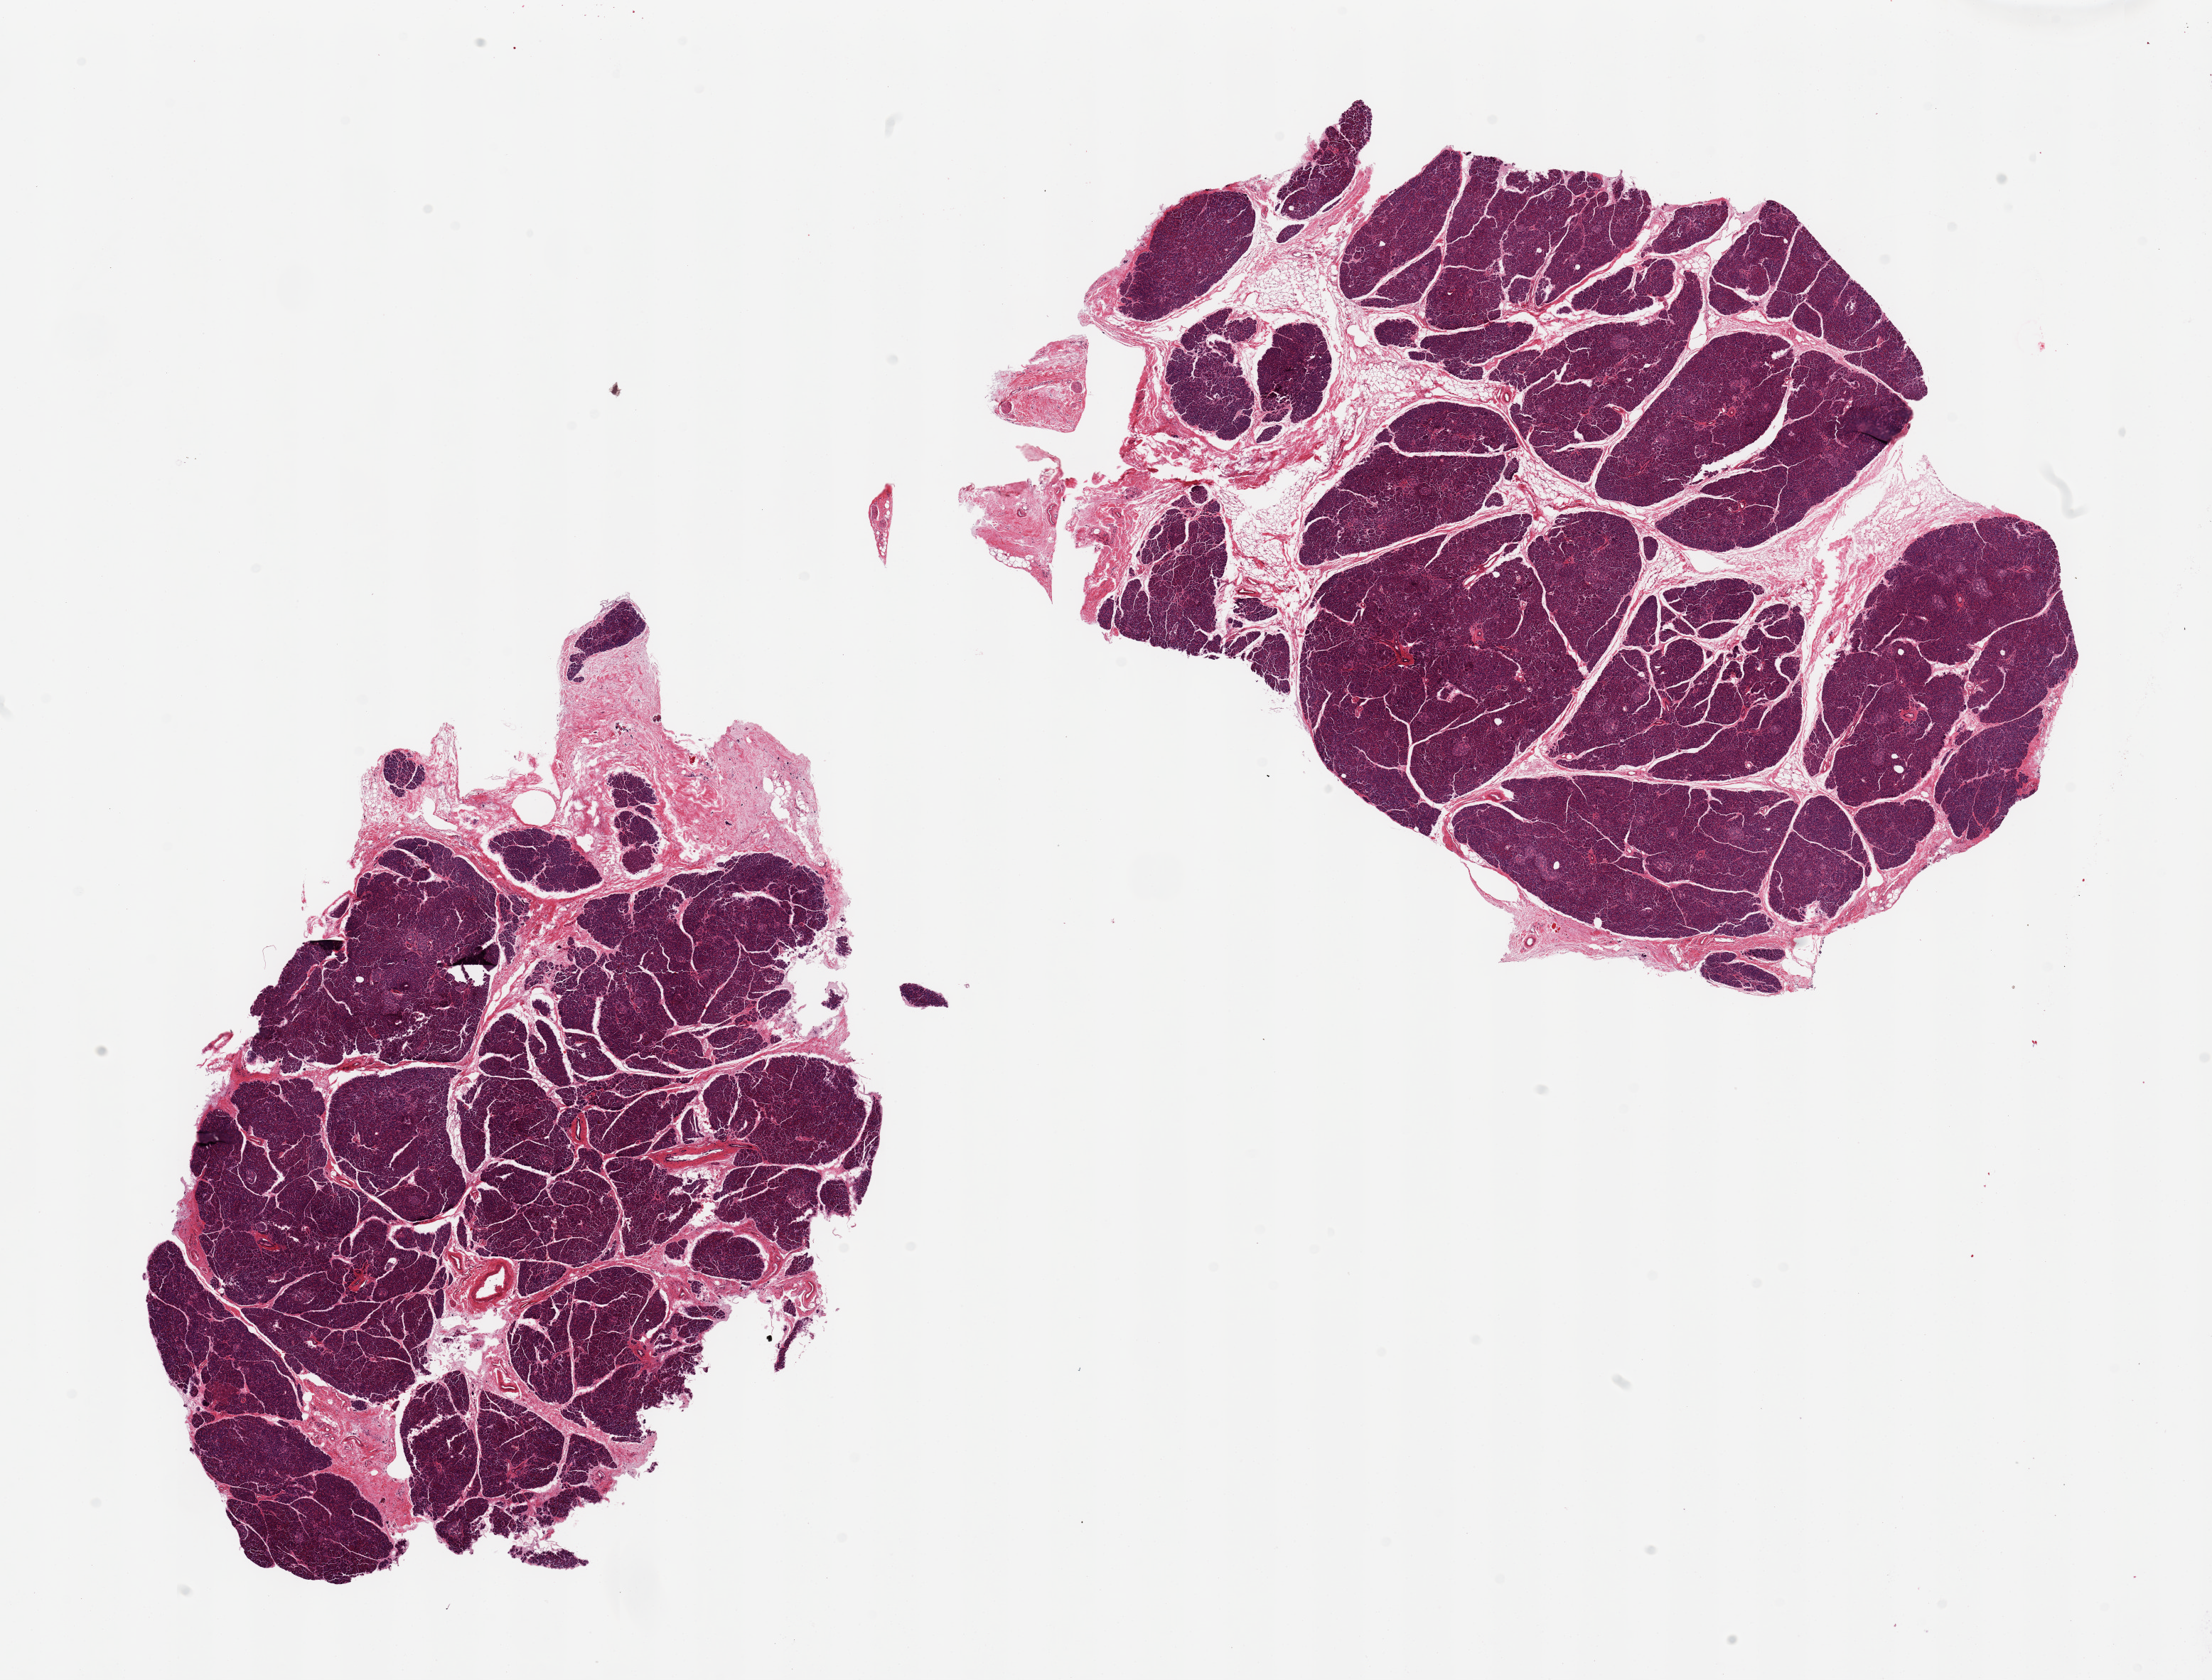
Digitized haematoxylin and eosin-stained section, brightfield, a low-resolution overview of the entire scanned area, about 24.6 x 18.7 mm; PAXgene-fixed paraffin-embedded (PFPE) section; section of pancreas (target tissue); tissue donor sample.
- pathologist's review note for this sample: 2 pieces; well preserved, islets well visualized, ~20% is fibrofatty tissue